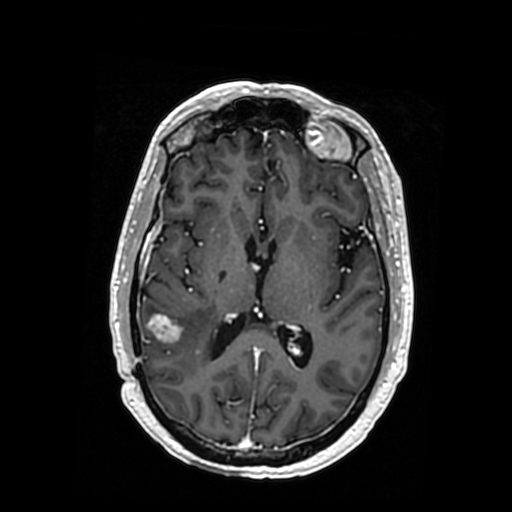
Brain MRI from a brain-tumour surgery series, one axial slice; position 176 of 364 along the scan axis; T1-weighted post-contrast; 0.5 mm slice thickness; 512 × 512 image matrix. Case-level facts recorded for this patient, not image findings: histopathology: Oligodendroglioma; WHO grade: 3; IDH mutation: yes.
Structures marked on this image (manually delineated by an expert):
- tumour: bounding box (x1, y1, x2, y2) in pixels: (158, 315, 209, 372)